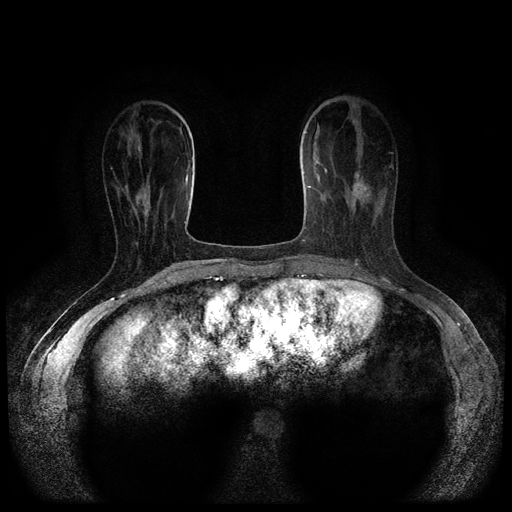
Breast MRI (dynamic contrast-enhanced, multi-phase), one axial slice; slice 31 of 116 in the series (ordered by position); dynamic contrast-enhanced series, time point 2 of 5 at this slice position (early post-contrast); 1.5 T; TE 2.6 ms, TR 5.4 ms; 2 mm slice thickness; 512 × 512 image matrix, field of view 340 × 340 mm. Female patient, age 47 years.
Structures marked on this image (semi-automatic segmentation, software-assisted and operator-edited):
- breast lesion (labelled 'tumour' in the annotation; benign lesions carry a separate 'benign' label): bounding box <350,172,370,214> (left, top, right, bottom; pixels)
- breast lesion (labelled 'tumour' in the annotation; benign lesions carry a separate 'benign' label): <135,194,151,226>